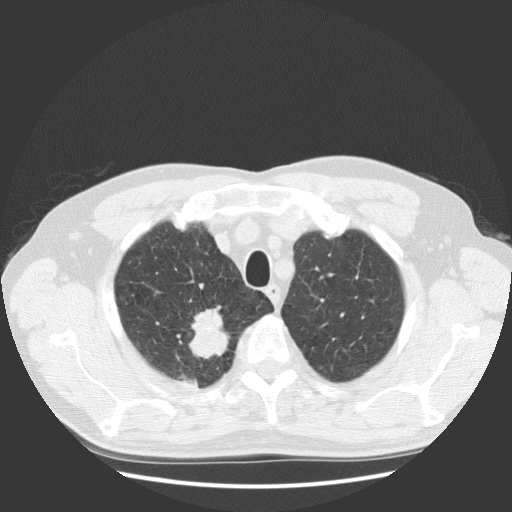
Low-dose screening chest CT, one axial slice. Slice 107 of 131 in the series (ordered by position). 140 kVp. Lung window (W 1500 / L -600 HU). 2.5 mm slice thickness. 512 × 512 image matrix.
Annotated regions visible in this slice (expert manual segmentation):
- lesion 1 (tumor, upper lobe of right lung): bounding box (x1, y1, x2, y2) in pixels: (189, 307, 230, 359)
- lesion 2 (tumor, upper lobe of right lung): (184, 376, 198, 388)